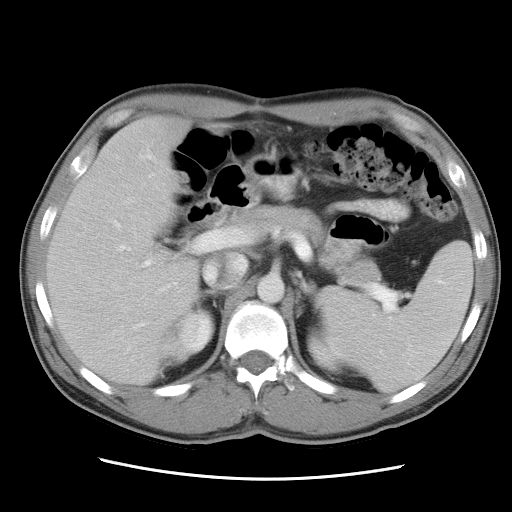
Contrast-enhanced abdominal CT, one axial slice. Position 18 of 34 along the scan axis. Reconstruction kernel STANDARD. 120 kVp. Soft-tissue window (W 400 / L 40 HU). 512 × 512 image matrix. Male patient, age 40 years. From the clinical record (not read from this slice): diagnosis: colorectal cancer liver metastases, imaged before liver resection; multiple liver metastases: yes; largest metastasis: 1.5 cm; disease in both lobes: yes.
Structures marked on this image (manually delineated by an expert):
- liver: bounding box [x1, y1, x2, y2] px = [48, 115, 200, 384]
- planned liver remnant (the part of the liver to remain after resection): [48, 115, 200, 384]
- portal vein (with intrahepatic branches): [114, 223, 247, 328]